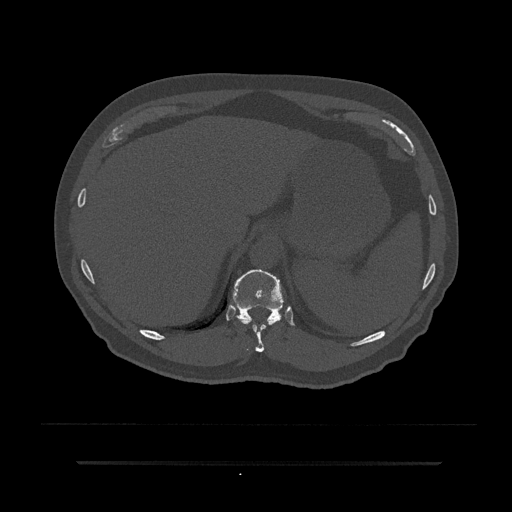
CT including the spine, one axial slice. Slice 295 of 797 in the series (ordered by position). Bone window (W 1800 / L 400 HU). 0.5 mm slice thickness. 512 × 512 image matrix, field of view 464 × 464 mm. Male patient, age 59 years. Case-level facts recorded for this patient, not image findings: primary cancer: bile ducts; vertebrae with lytic lesions (as recorded): T10.
Annotated regions visible in this slice (semi-automatically segmented with operator editing):
- T10 vertebra: bounding box <234,282,281,352> (left, top, right, bottom; pixels)
- T11 vertebra: <229,269,288,323>